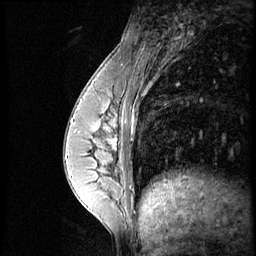
Breast MRI (dynamic contrast-enhanced), one sagittal slice. Slice 20 of 56 in the series (ordered by position). Dynamic contrast-enhanced series, image 2 of 4 at this slice position (ordered by acquisition). 1.5 T. TE 4.2 ms, TR 8.9 ms. 2.5 mm slice thickness. 256 × 256 image matrix, field of view 200 × 200 mm. Female patient, age 35 years. Case-level facts recorded for this patient, not image findings: setting: breast cancer imaged before/during neoadjuvant chemotherapy; receptor status: HER2-positive.
Annotated regions visible in this slice (semi-automatically segmented with operator editing):
- analysis volume of interest (the breast-tissue region the enhancement analysis was run in; not a lesion): bounding box (x1, y1, x2, y2) in pixels: (73, 111, 131, 164)
- tumour enhancement mask (voxels above the 140 % enhancement threshold inside the analysis volume of interest): (112, 115, 118, 149)